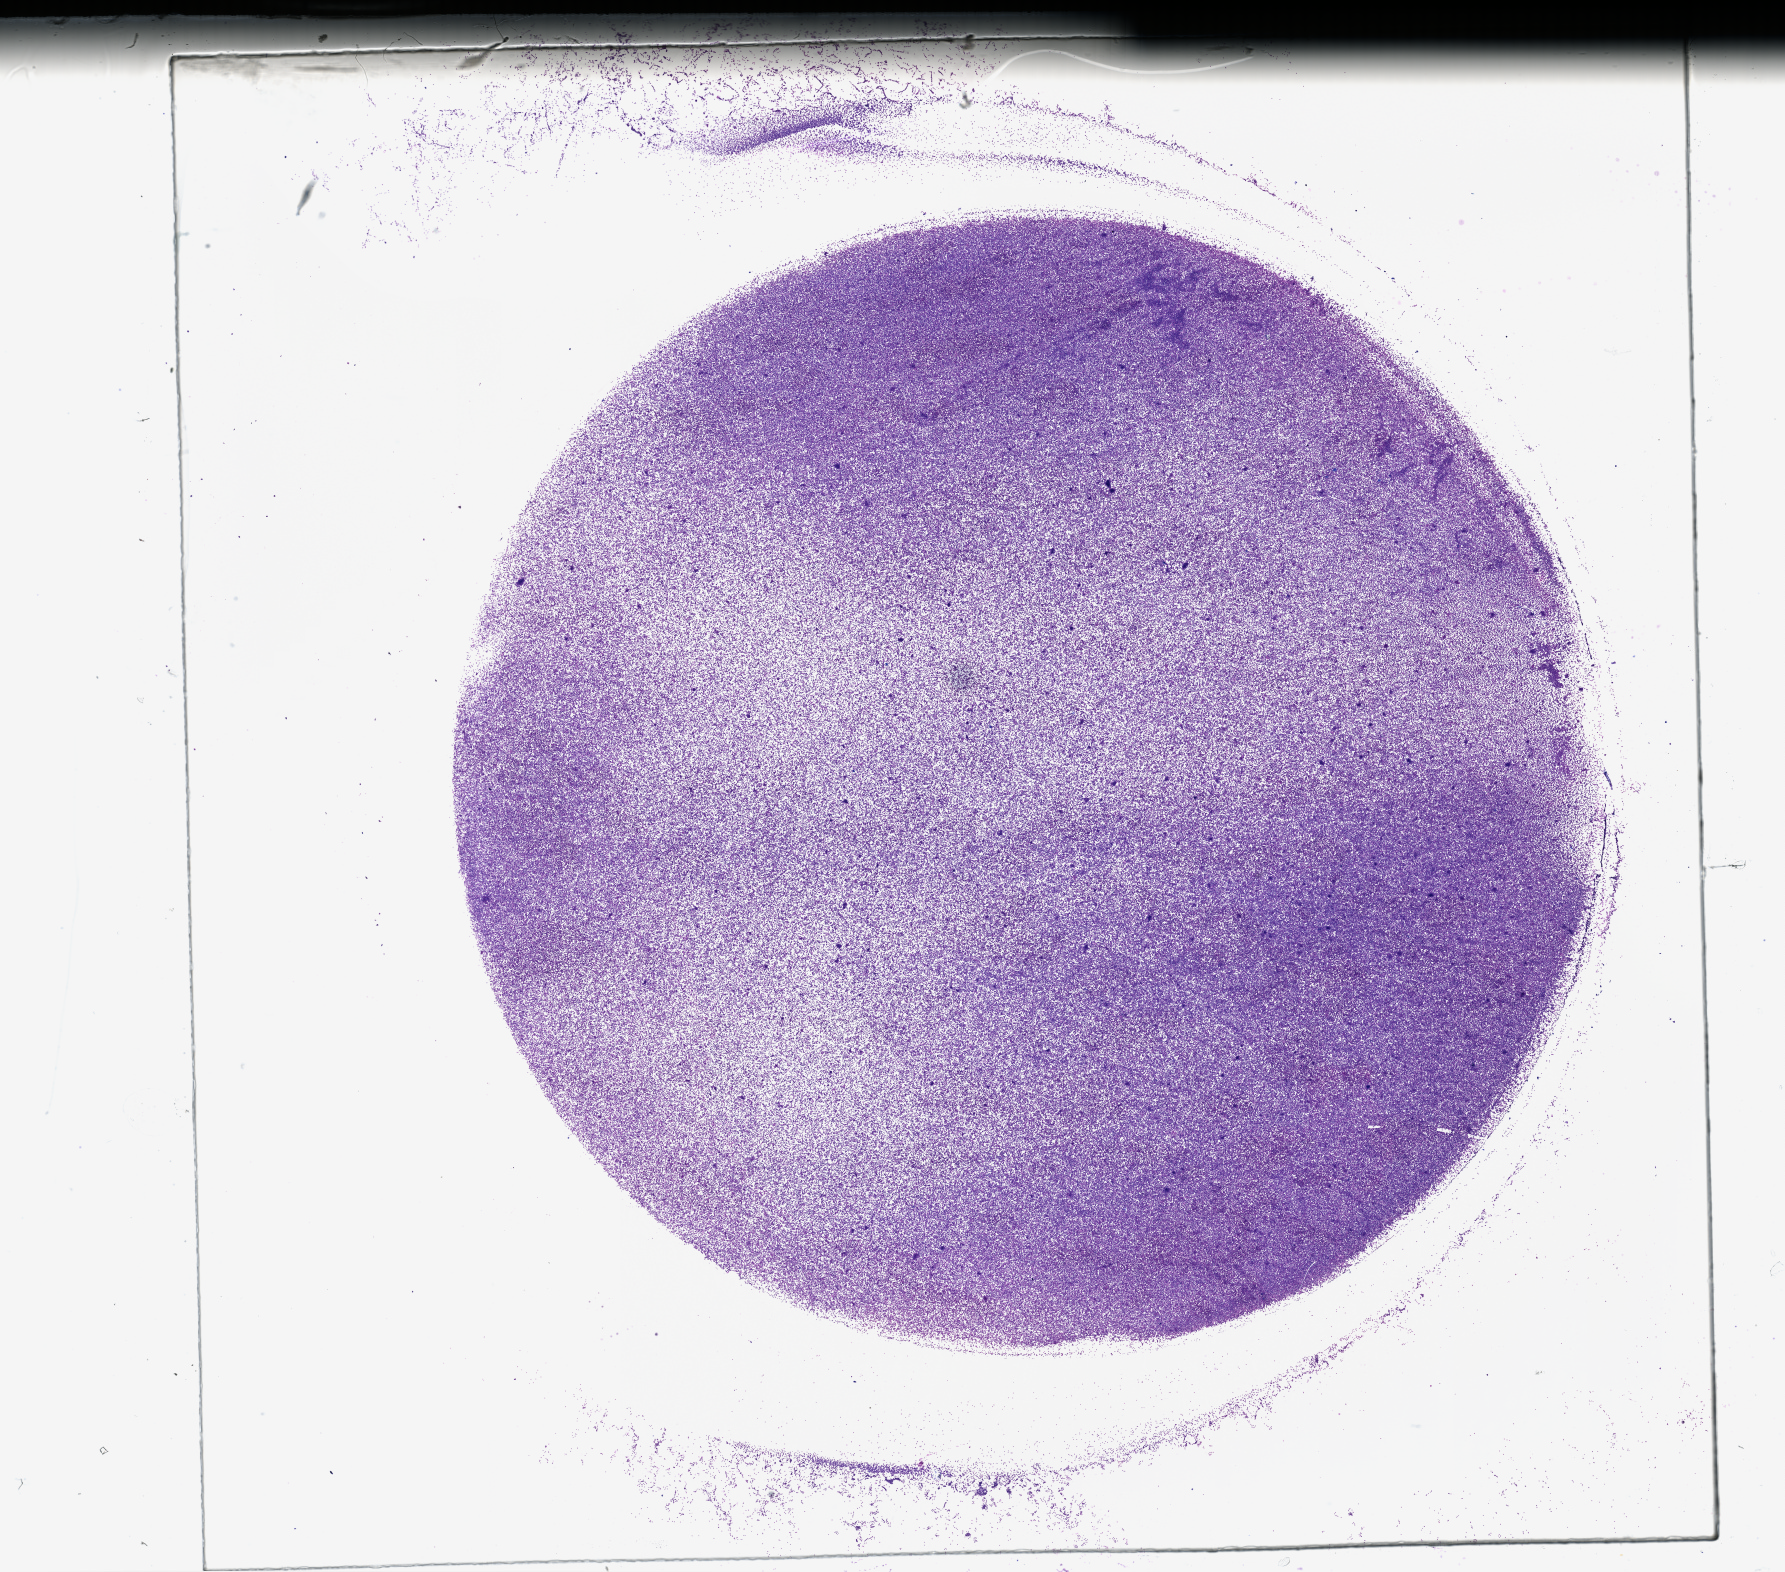
Digitized H&E-stained tissue section (whole slide) — shown as a low-resolution overview of the whole scanned area (about 28.2 x 24.8 mm), bone marrow (leukaemic) sample. Female, 71 y/o.
Diagnosis: Acute Myeloid Leukemia.